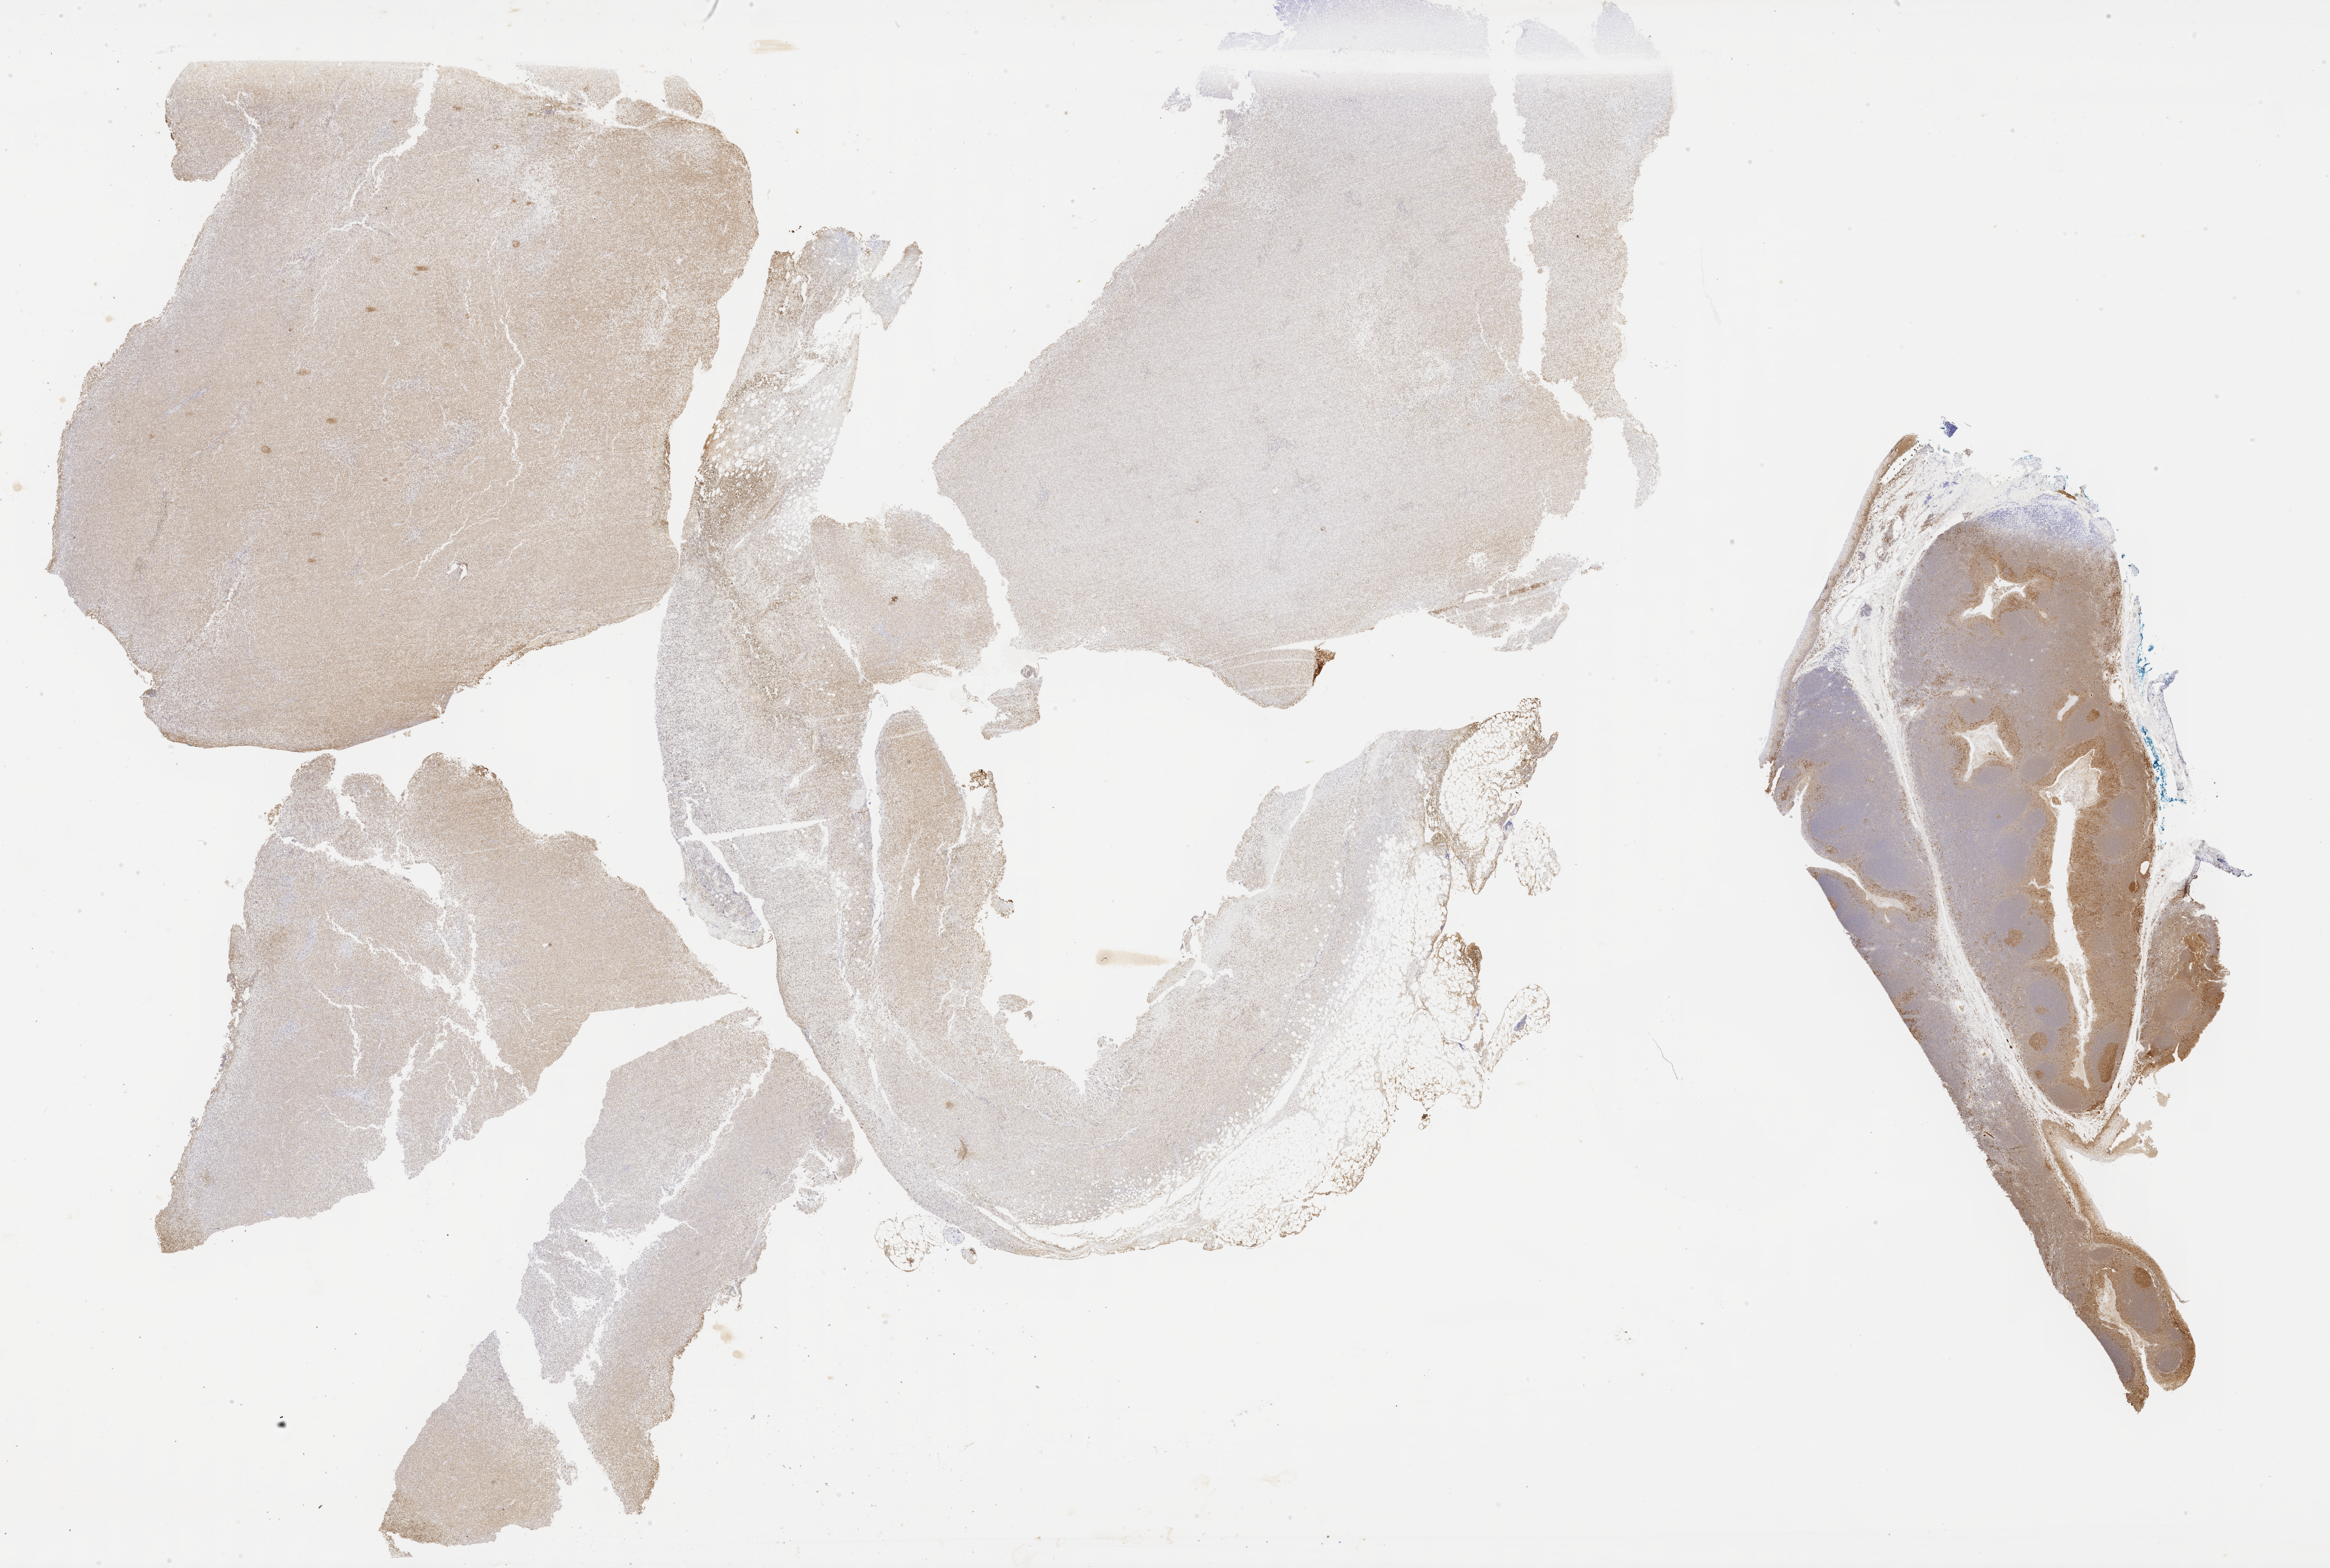
Whole-slide image, immunohistochemical stain for BCL6, shown as a low-resolution overview of the whole scanned area (about 32.7 x 22.0 mm). Female patient.
Specimen: tumor tissue.